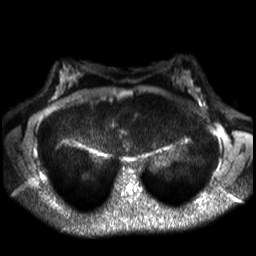
Breast MRI, one axial slice; slice 21 of 30 in the series (ordered by position); diffusion-weighted series; image 2 of 4 stored at this slice position (different b-values; order by instance number); 3 T; 256 × 256 image matrix. Female patient.
Outlined on this slice (manually delineated by an expert):
- tumour on diffusion-weighted imaging: bounding box (x1, y1, x2, y2) in pixels: (193, 93, 200, 101)